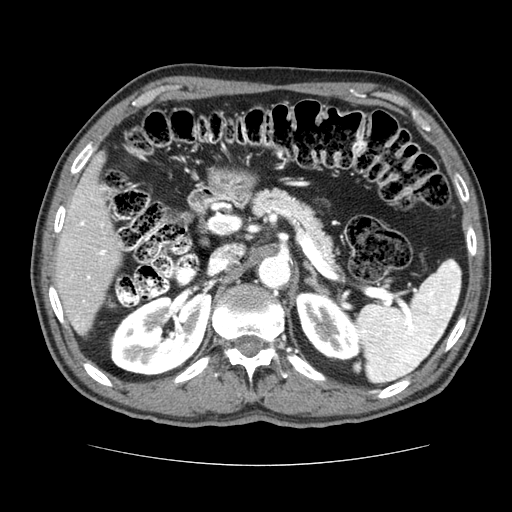
Contrast-enhanced abdominal CT (liver protocol), one axial slice; reconstruction kernel STANDARD; 120 kVp; soft-tissue window (W 400 / L 40 HU); 2.5 mm slice thickness; 512 × 512 image matrix, field of view 360 × 360 mm. From the clinical record (not read from this slice): diagnosis: hepatocellular carcinoma (patient treated with transarterial chemoembolisation; whether this scan precedes or follows treatment is not stated here); TNM stage (as recorded): Stage-I; Child-Pugh class: A.
Outlined on this slice (semi-automatically segmented with operator editing):
- liver parenchyma outside the tumour (the mass and vessels are separate outlines, so this box may not span the whole liver): bounding box (x1, y1, x2, y2) in pixels: (54, 154, 122, 334)
- liver vessels: (65, 197, 106, 329)